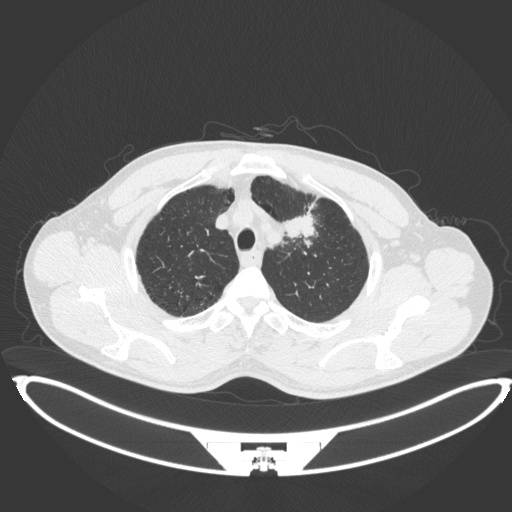
Chest CT, one axial slice. Position 365 of 407 along the scan axis. Reconstruction kernel B31f. 120 kVp. Lung window (W 1500 / L -600 HU). 1 mm slice thickness. 512 × 512 image matrix, field of view 457 × 457 mm. Patient: male, 60 years. From the clinical record (not read from this slice): clinical TNM (as recorded): T2a N0 M0.
Annotated regions visible in this slice (rectangle marked by the reading radiologist):
- lung tumour (recorded histology: squamous cell carcinoma): bounding box (x1, y1, x2, y2) in pixels: (279, 208, 318, 240)